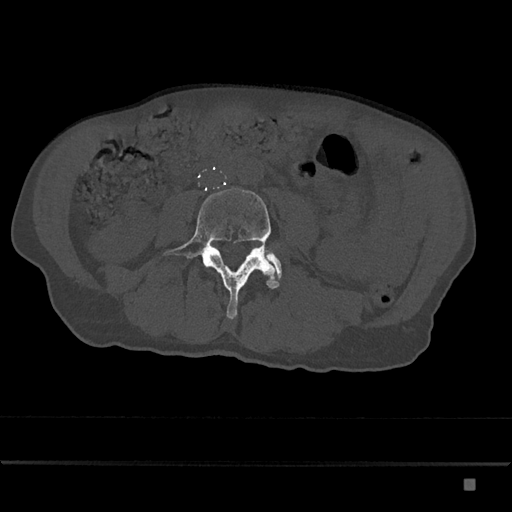
CT including the spine, one axial slice; slice 337 of 797 in the series (ordered by position); reconstruction kernel Br40s/3; bone window (W 1800 / L 400 HU); 512 × 512 image matrix. Male patient, age 72 years. Case-level facts recorded for this patient, not image findings: primary cancer: prostate.
Structures marked on this image (semi-automatic segmentation, software-assisted and operator-edited):
- L4 vertebra: bounding box <162,188,282,319> (left, top, right, bottom; pixels)
- L5 vertebra: <267,254,282,273>